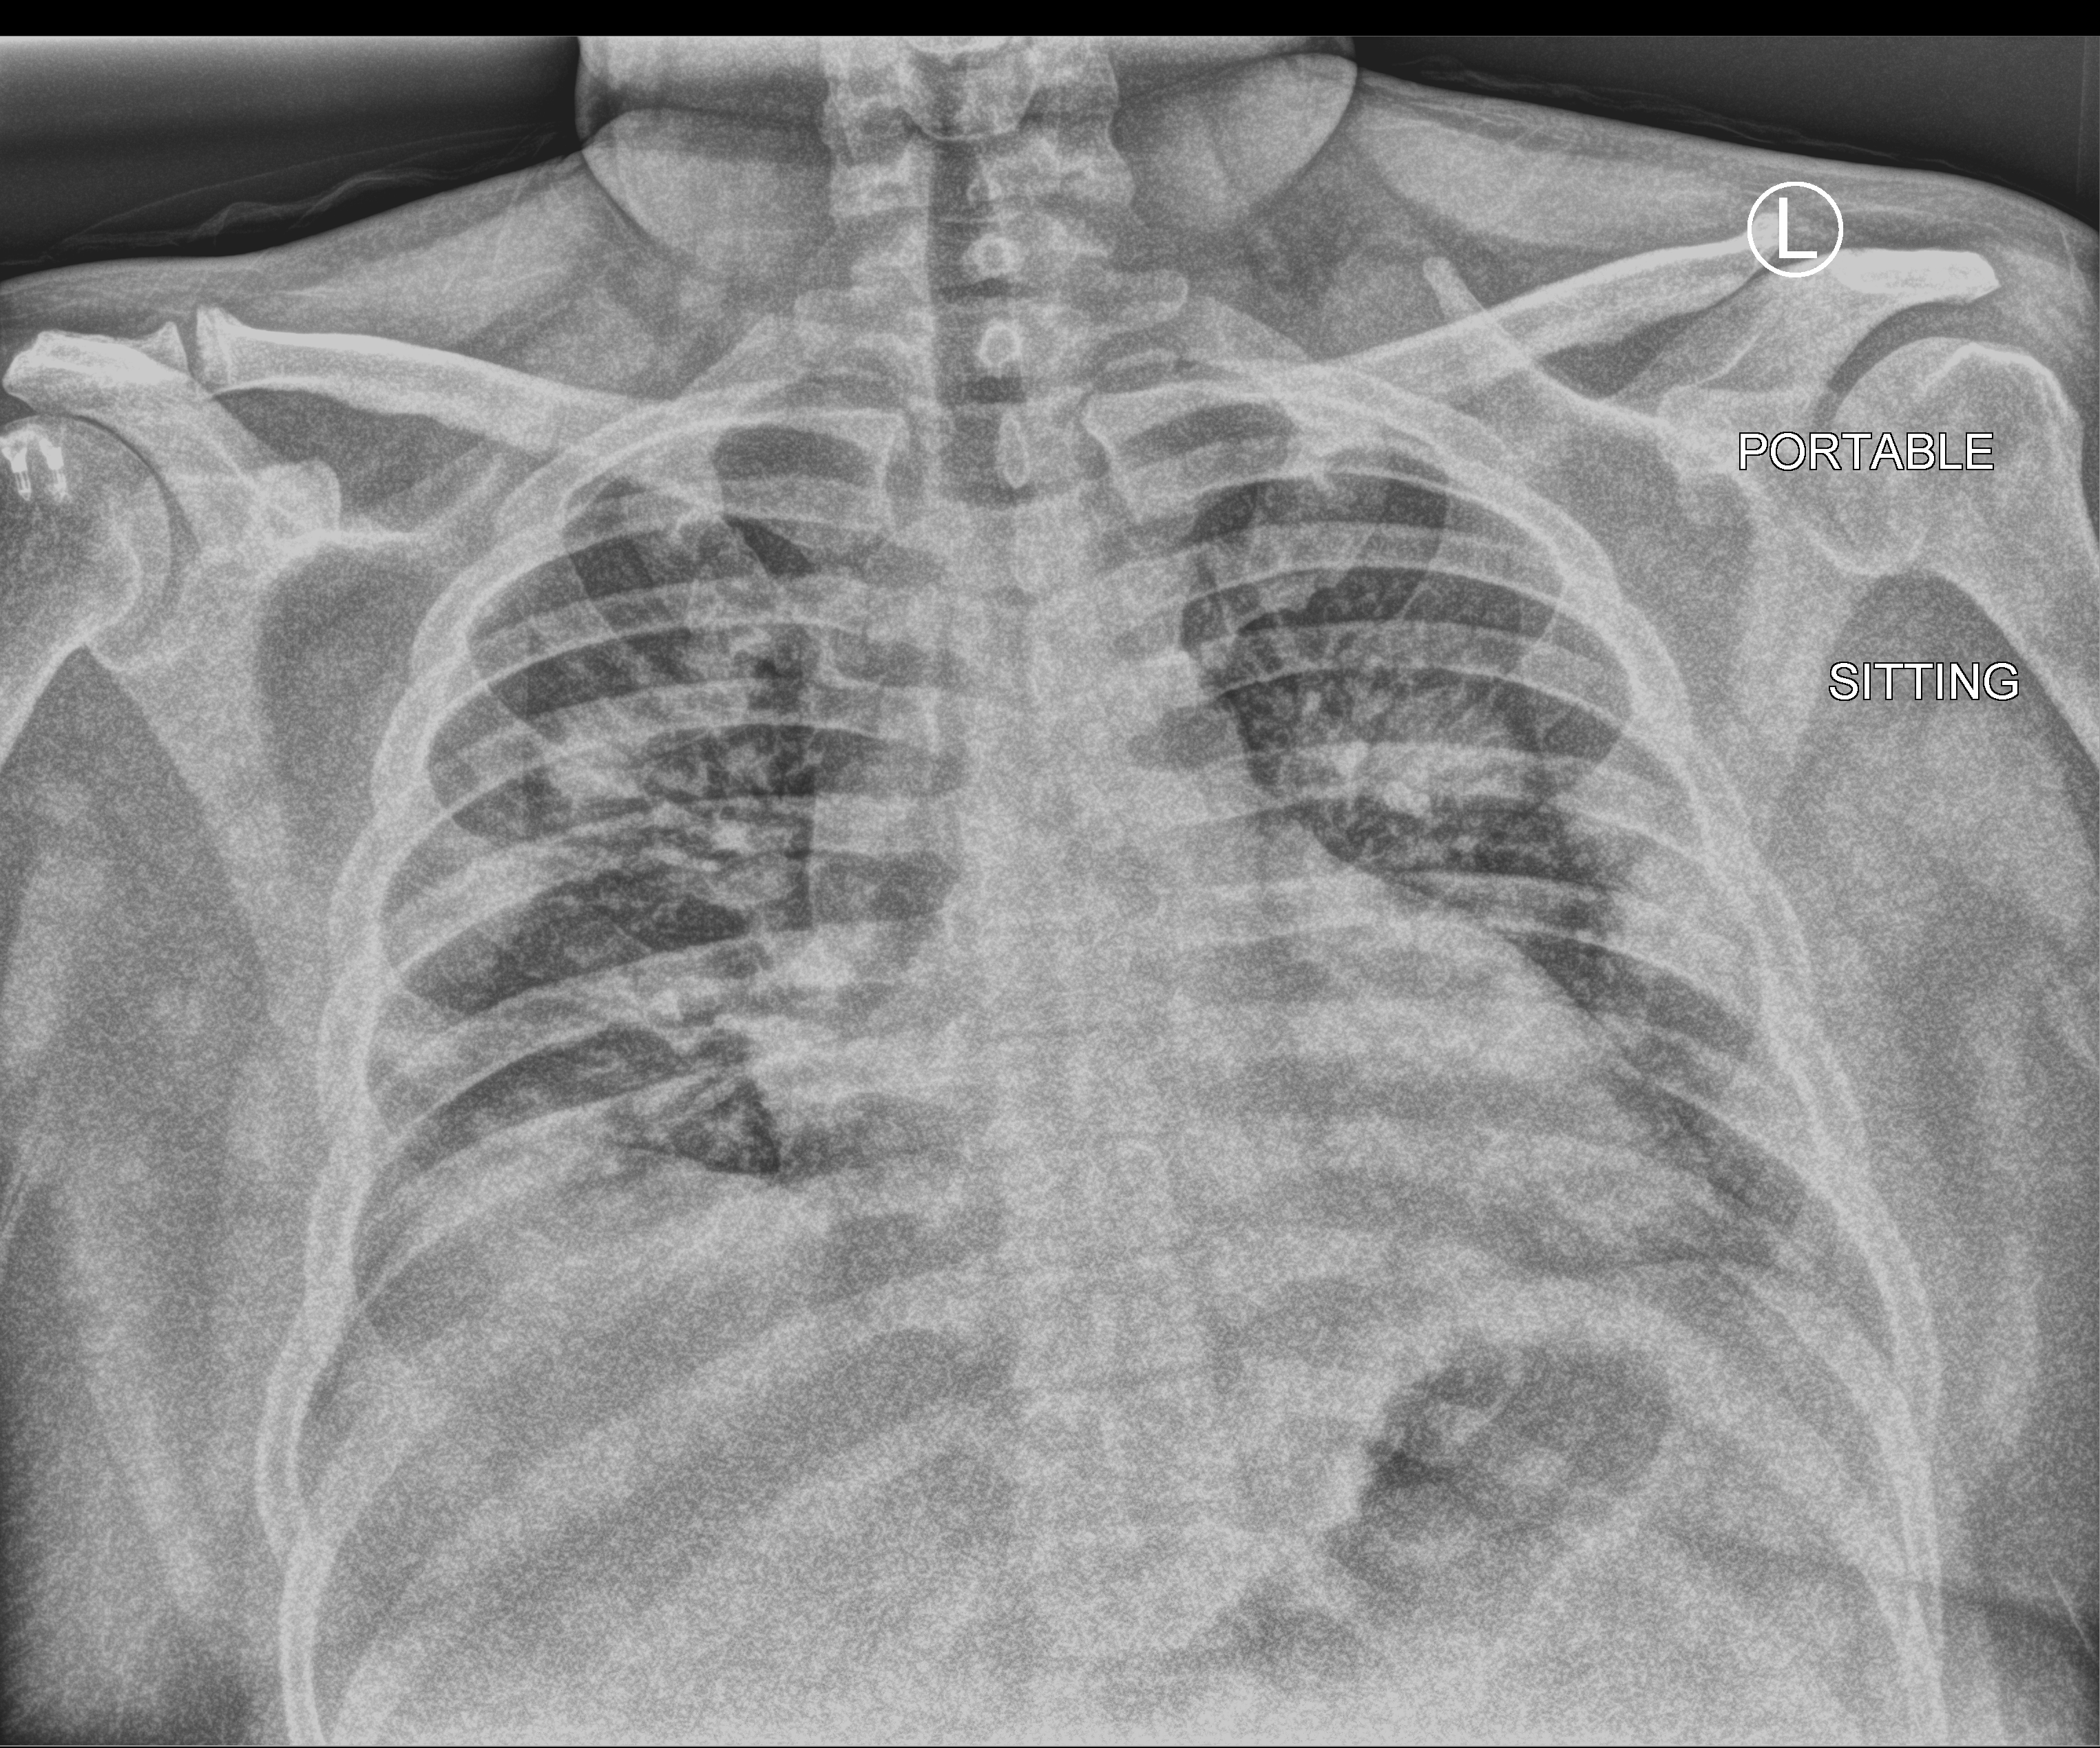
Bedside chest radiograph (computed radiography). Patient hospitalised with COVID-19; male, aged 18–59 years.
Admission-level facts for this patient (not findings on this image; timing relative to this image not recorded): admitted to intensive care during this hospital stay: no; mechanically ventilated during this hospital stay: no.